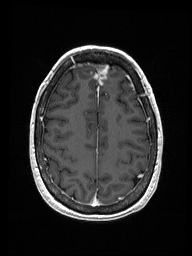
Brain MRI from a brain-tumour surgery series, one axial slice; position 47 of 192 along the scan axis; T1-weighted post-contrast; 1 mm slice thickness; 192 × 256 image matrix. Case-level facts recorded for this patient, not image findings: histopathology: Metastastic Carcinoma from Breast primary; tumour location: Right Frontal.
Outlined on this slice (outlined manually by an expert reader):
- previous resection cavity: box from (x=96, y=64) to (x=109, y=84) px